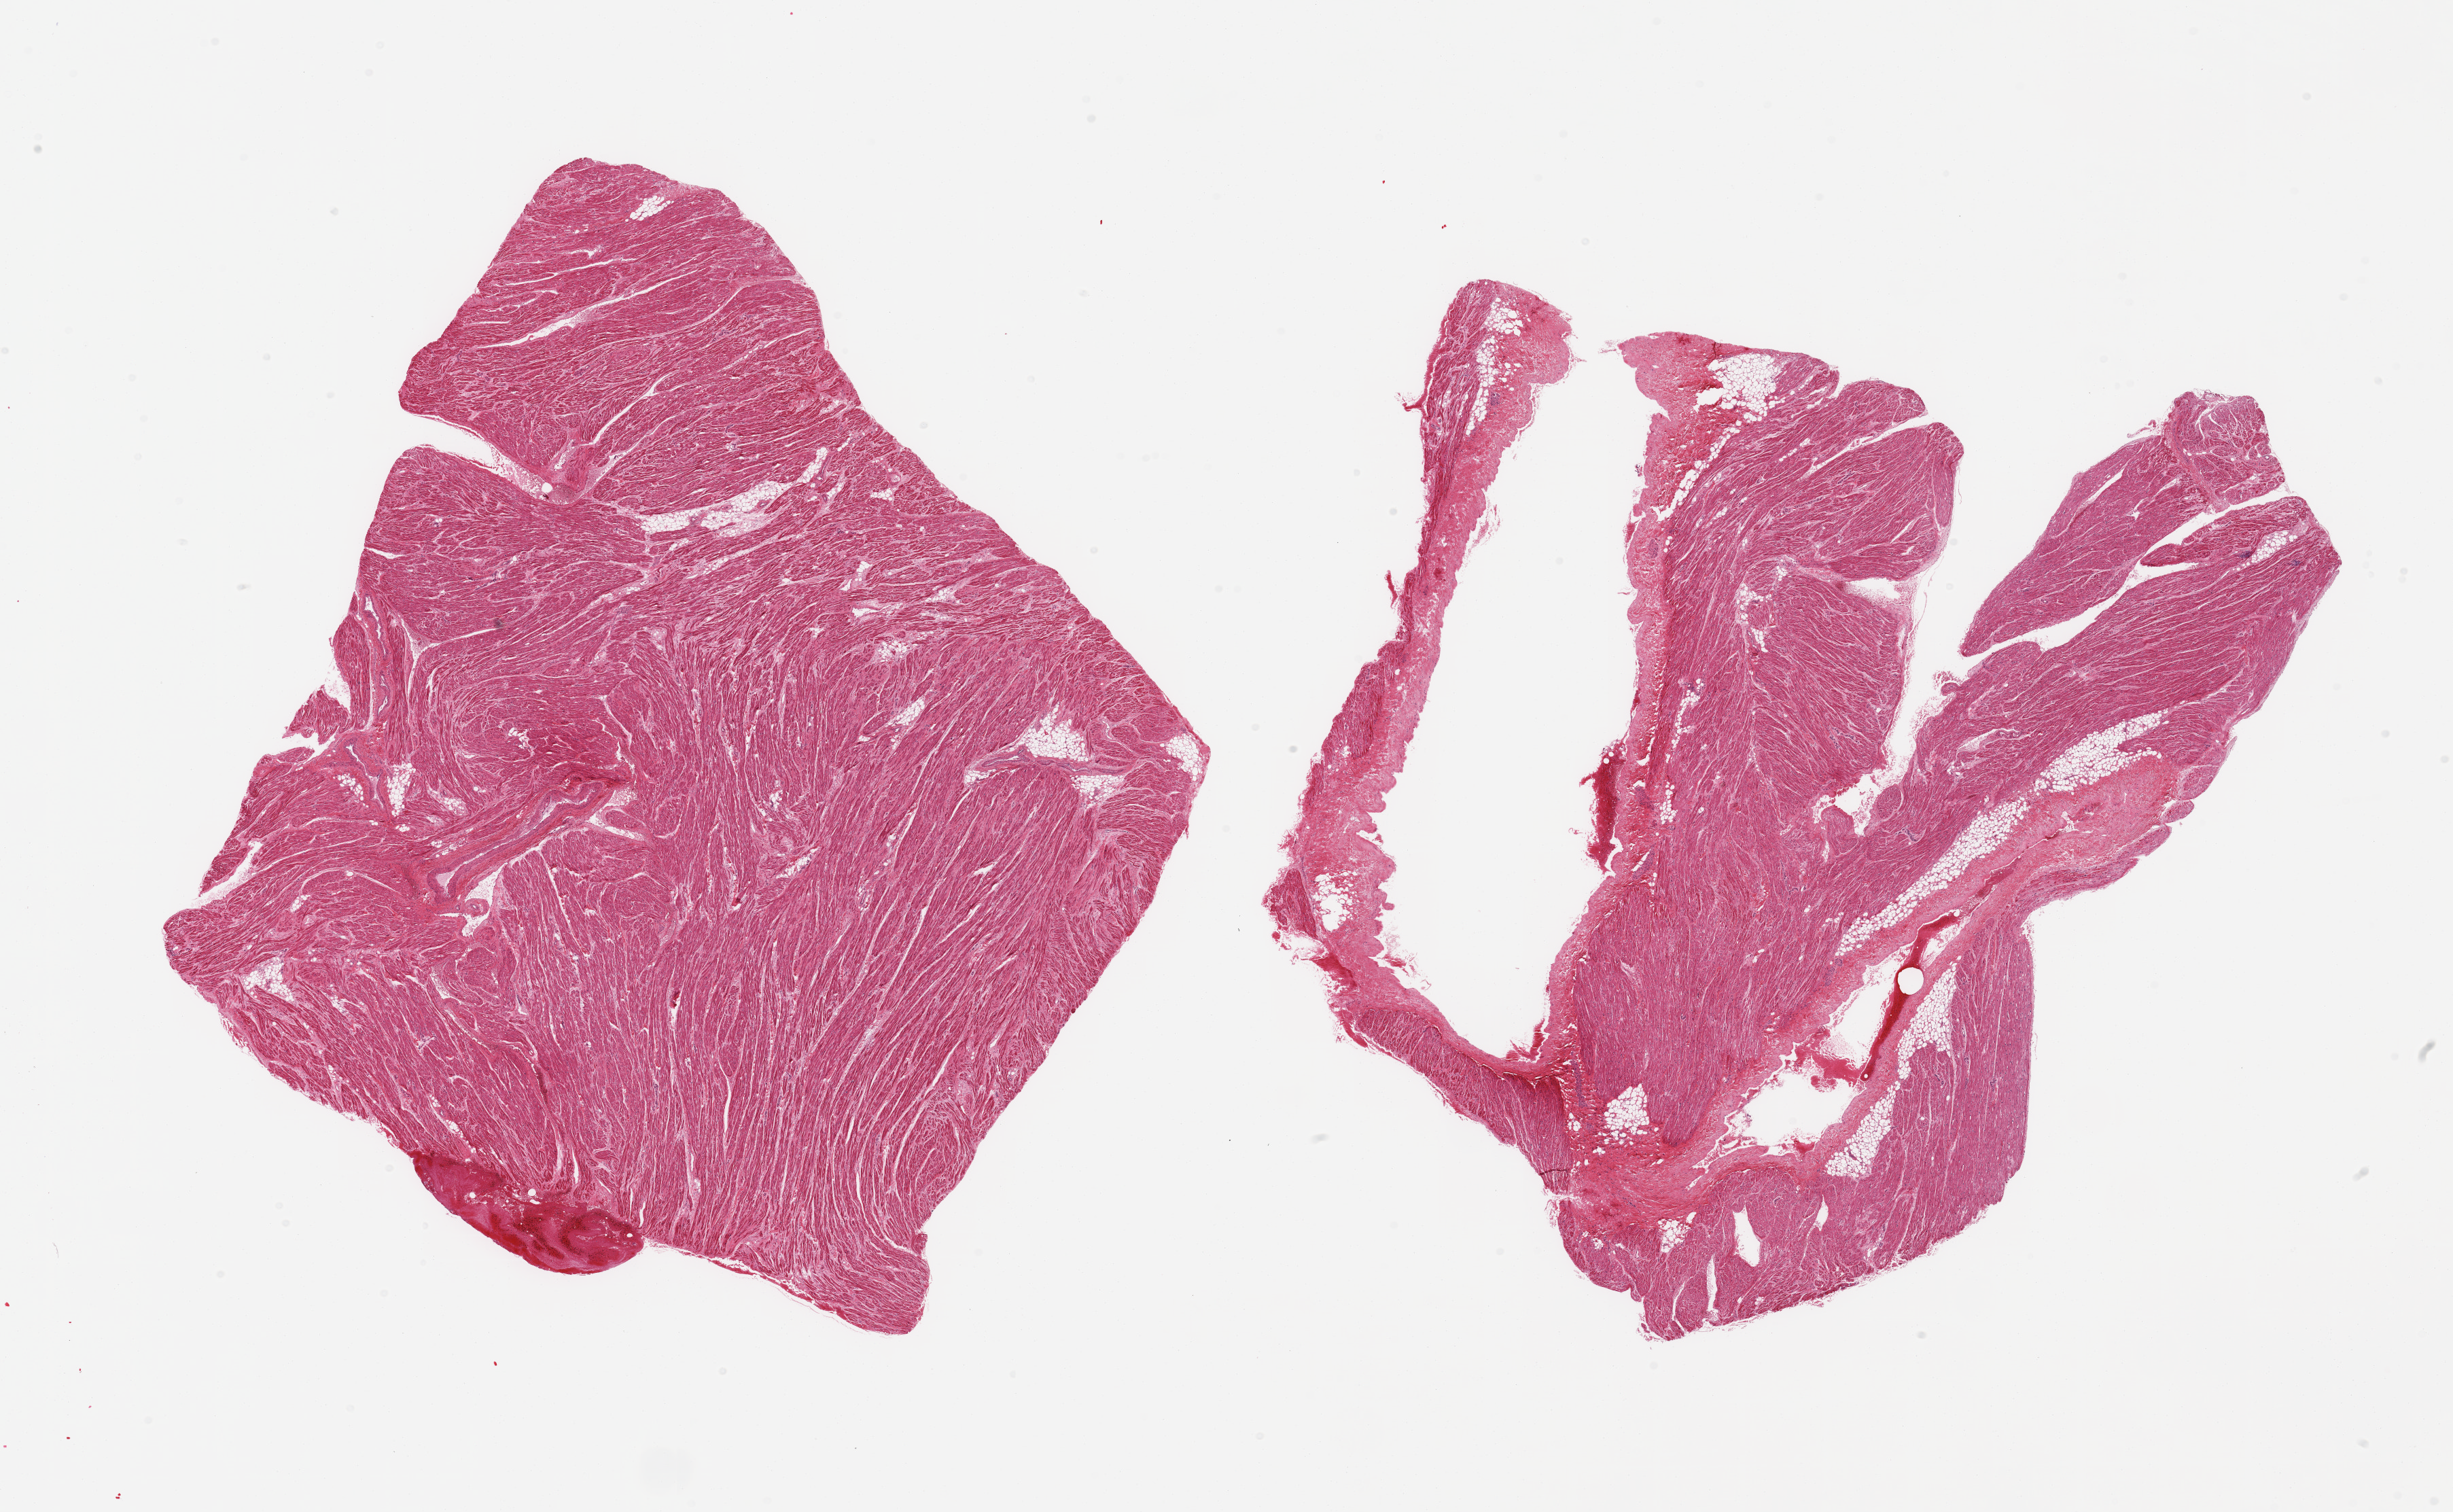
H&E whole-slide image, a low-resolution overview of the entire scanned area, about 28.5 x 17.6 mm; PAXgene-fixed, paraffin-embedded tissue; section of auricular appendage (target tissue); tissue donor sample.
Pathologist's review note for this sample: 2 pieces; scattered fat, interstitial fibrosis.